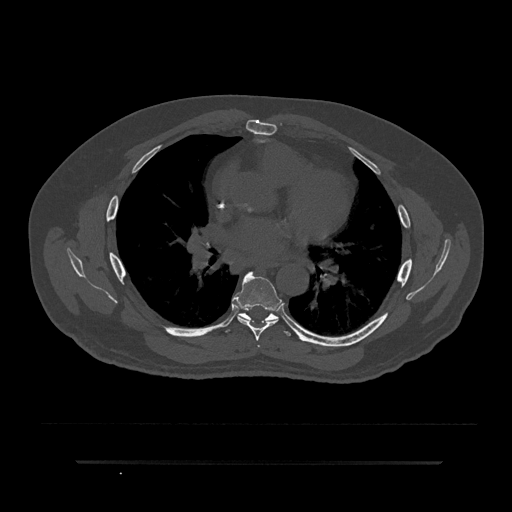
CT including the spine, one axial slice. Slice 510 of 797 in the series (ordered by position). 120 kVp. Bone window (W 1800 / L 400 HU). 0.5 mm slice thickness. 512 × 512 image matrix, field of view 464 × 464 mm. Male patient, age 59 years. Case-level facts recorded for this patient, not image findings: primary cancer: bile ducts; vertebrae with lytic lesions (as recorded): T10.
Outlined on this slice (semi-automatic segmentation, software-assisted and operator-edited):
- T5 vertebra: bounding box <257,345,261,348> (left, top, right, bottom; pixels)
- T6 vertebra: <233,271,282,341>
- T7 vertebra: <225,313,295,336>